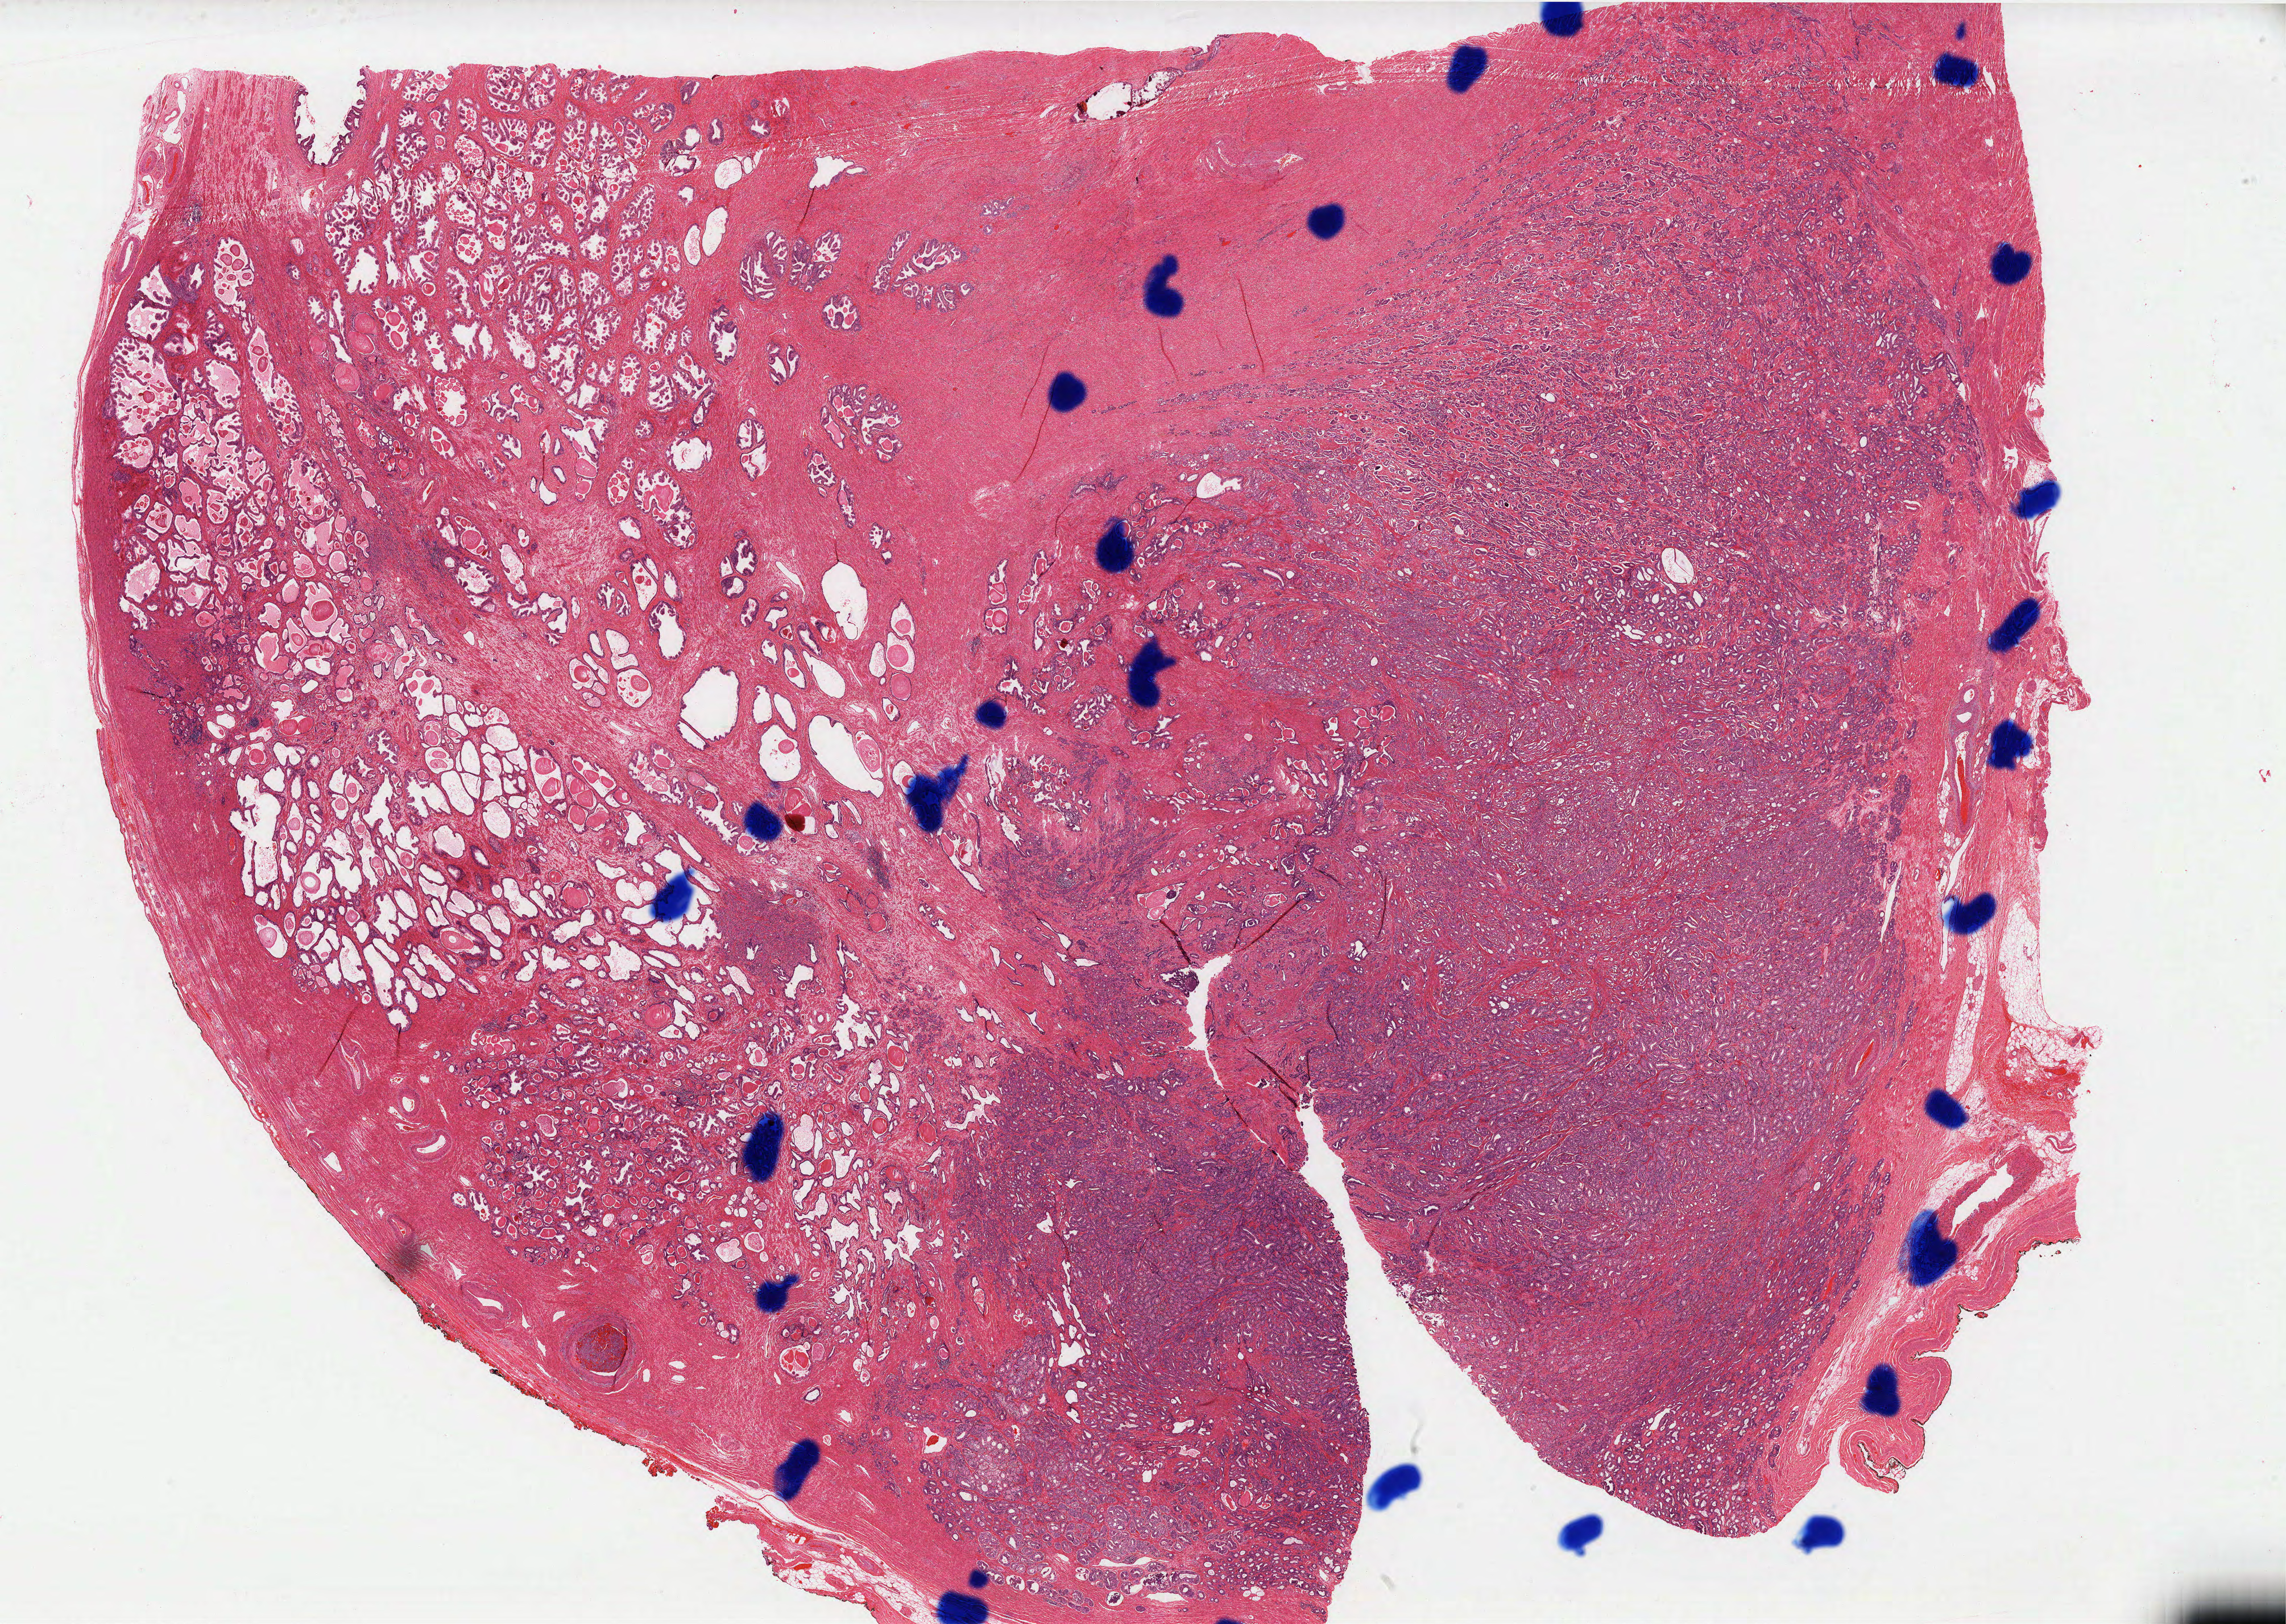
Digitized Hematoxylin and eosin (H&E) stained tissue section (whole slide) — shown as a low-resolution overview of the whole scanned area (about 32.2 x 22.9 mm, from a 40x scan); FFPE section; primary tumour sample from the prostate. Male, age 46 years at initial diagnosis. Gleason score: 8 (3+5).
- histologic diagnosis: Adenocarcinoma, NOS (prostate gland)
- laterality: bilateral